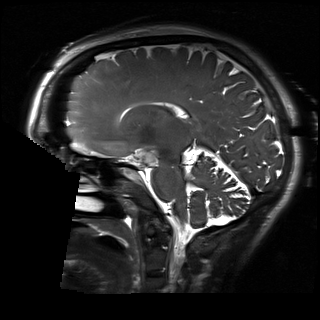
Brain MRI from a brain-tumour surgery series, one sagittal slice. 1 mm slice thickness. 320 × 320 image matrix, field of view 230 × 230 mm. Case-level facts recorded for this patient, not image findings: histopathology: Glioblastoma; WHO grade: 2; IDH mutation: no; tumour location: Right Skull Base Temporal.
Structures marked on this image (manually delineated by an expert):
- residual tumour: box from (x=138, y=149) to (x=157, y=163) px